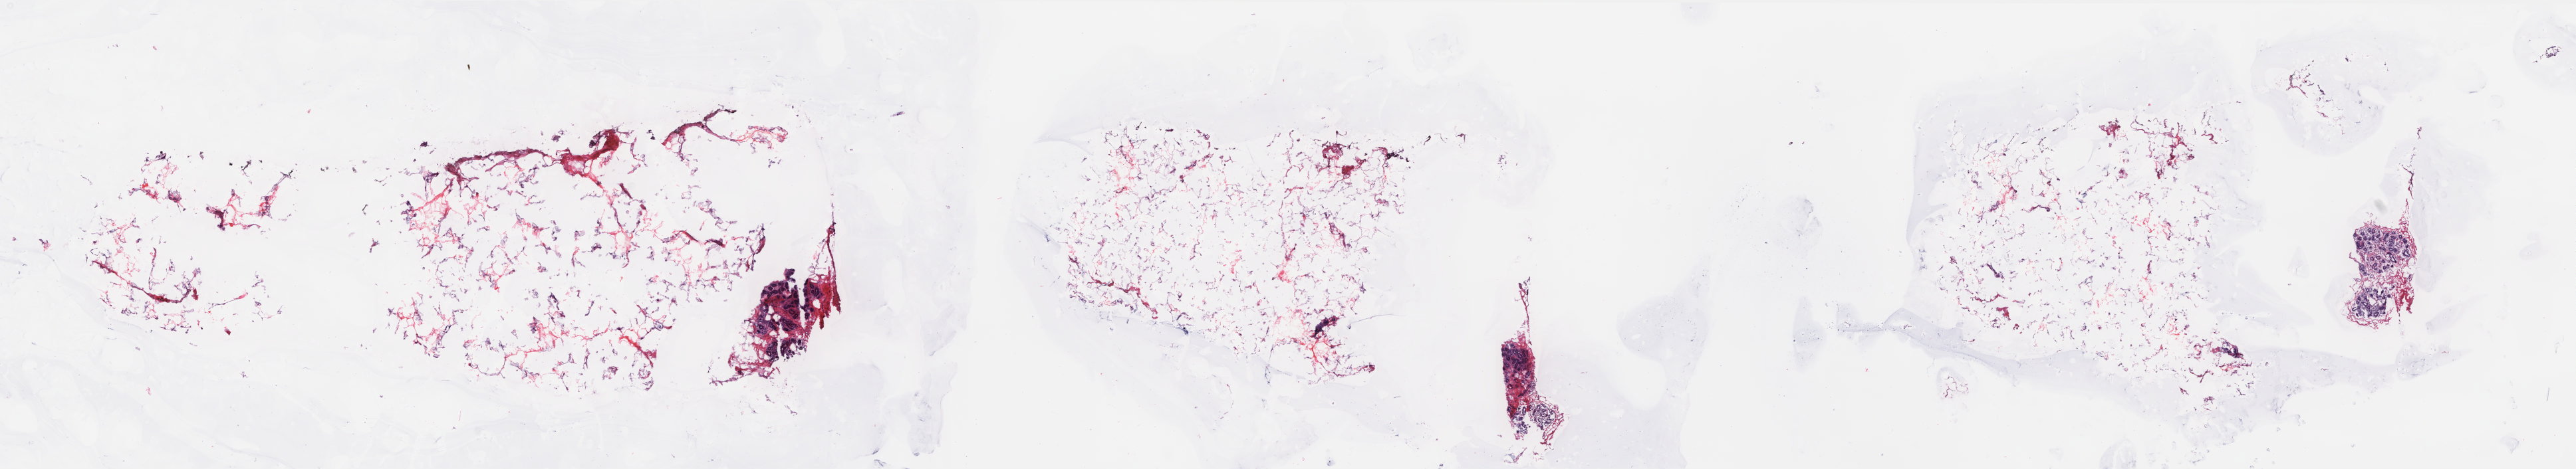
Whole-slide histology image, H&E — shown as a low-resolution overview of the whole scanned area (about 30.9 x 5.6 mm). Frozen section from the top of the tissue portion. Solid tissue normal (non-tumour tissue) sample from the breast. Female patient; age at initial diagnosis 45 years. Slide review estimates, as recorded: tumour cells 0%, tumour nuclei 0%, normal cells 7%, stromal cells 93%, necrosis 0%. Infiltration values recorded for this section: lymphocyte infiltration 2%, monocyte infiltration 0%, neutrophil infiltration 0%.
• this section: solid tissue normal (non-tumour) sample from the same patient
• patient diagnosis: Lobular carcinoma, NOS